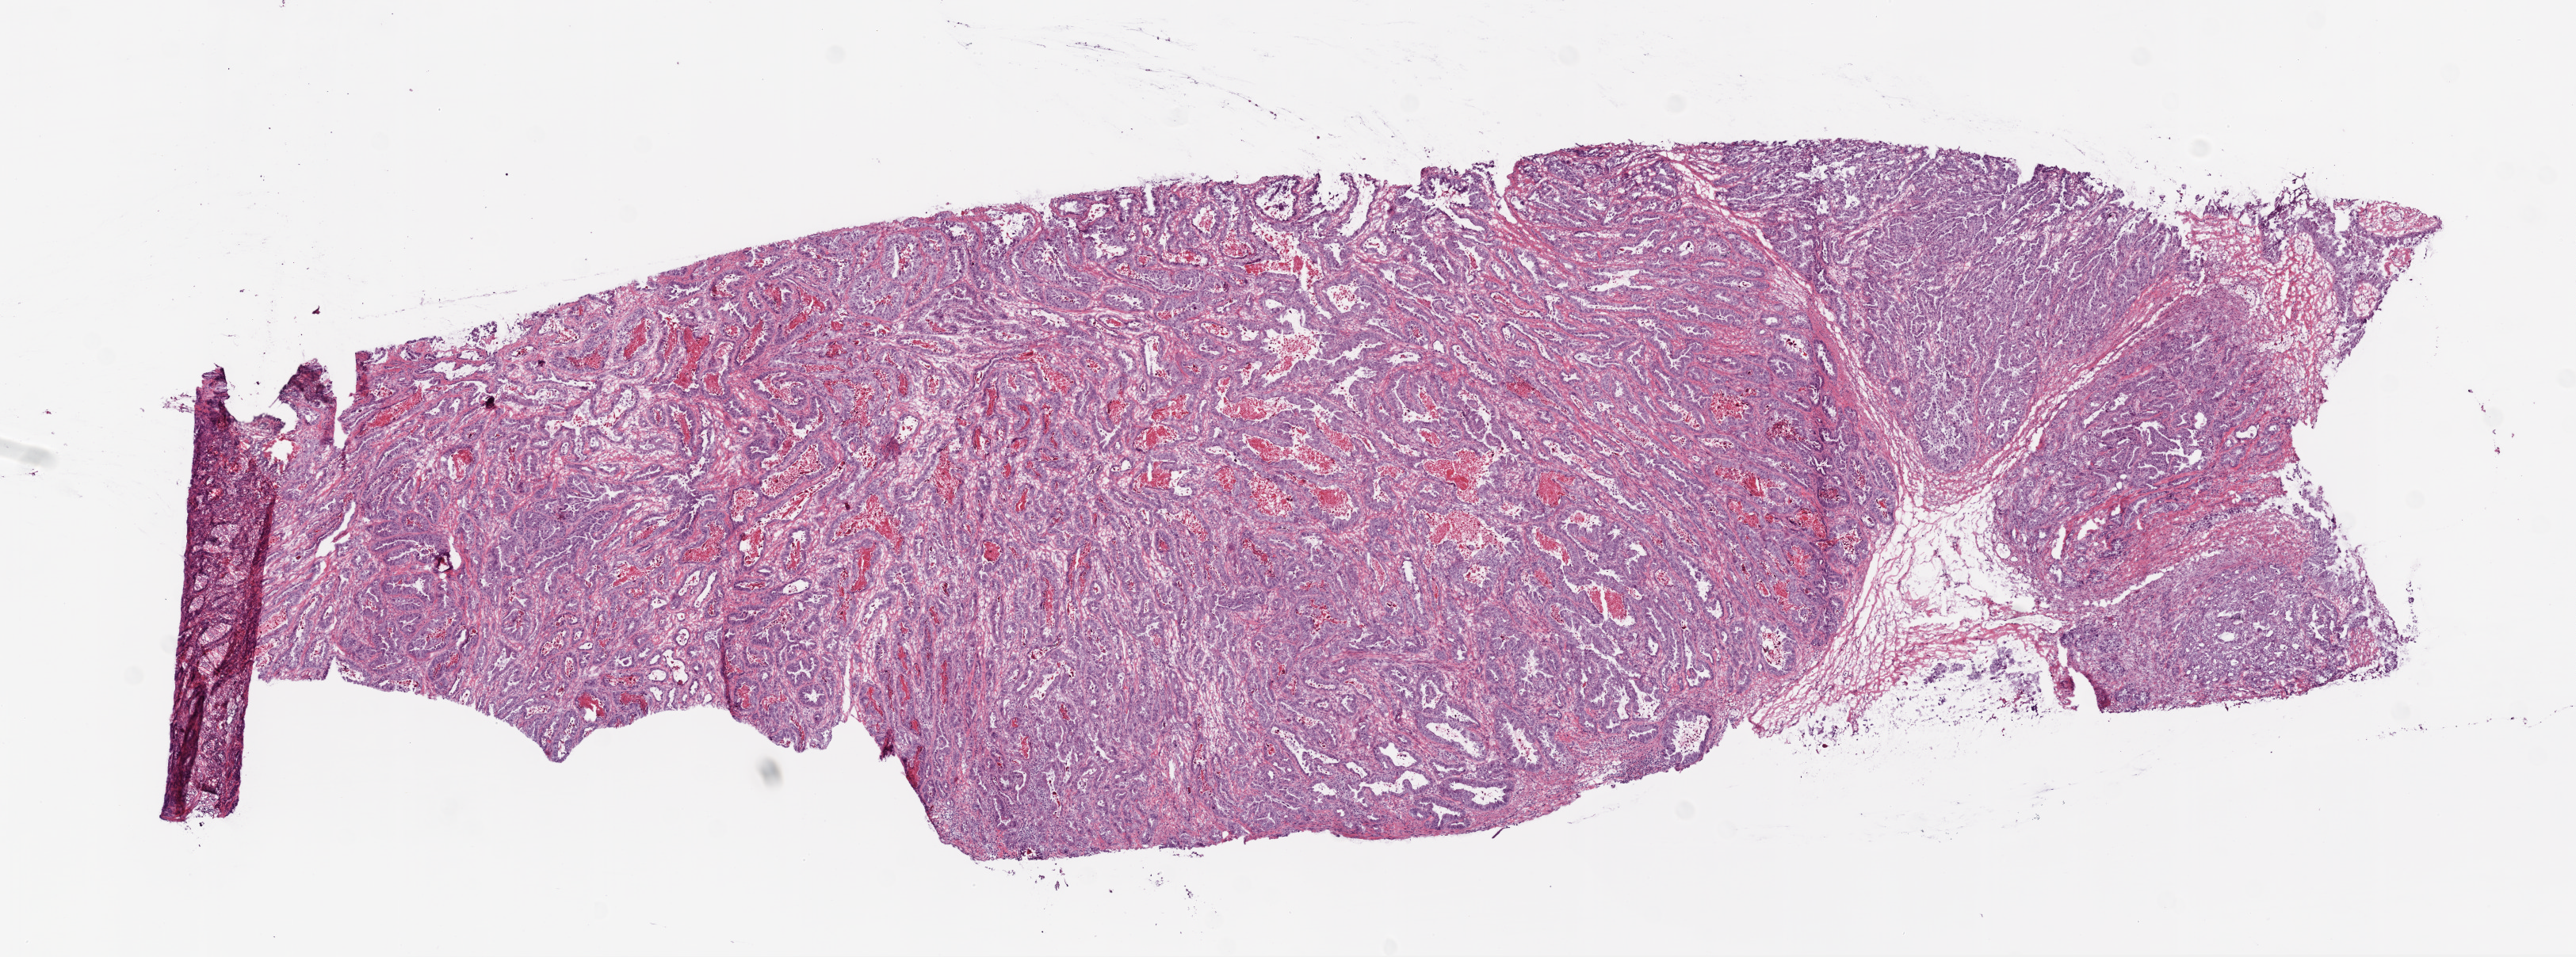
H&E whole-slide image — whole scanned area (about 13.0 x 4.8 mm) shown as a low-resolution overview; frozen section; sample: primary tumour, ovary. Female, age 60 years at initial diagnosis. Histologic grade: G3 (poorly differentiated). Composition of this section per pathologist review: tumour cells 80%, tumour nuclei 80%, normal cells 0%, stromal cells 20%, necrosis 0%.
FIGO stage: IIIC. Histologic diagnosis: Serous cystadenocarcinoma, NOS.